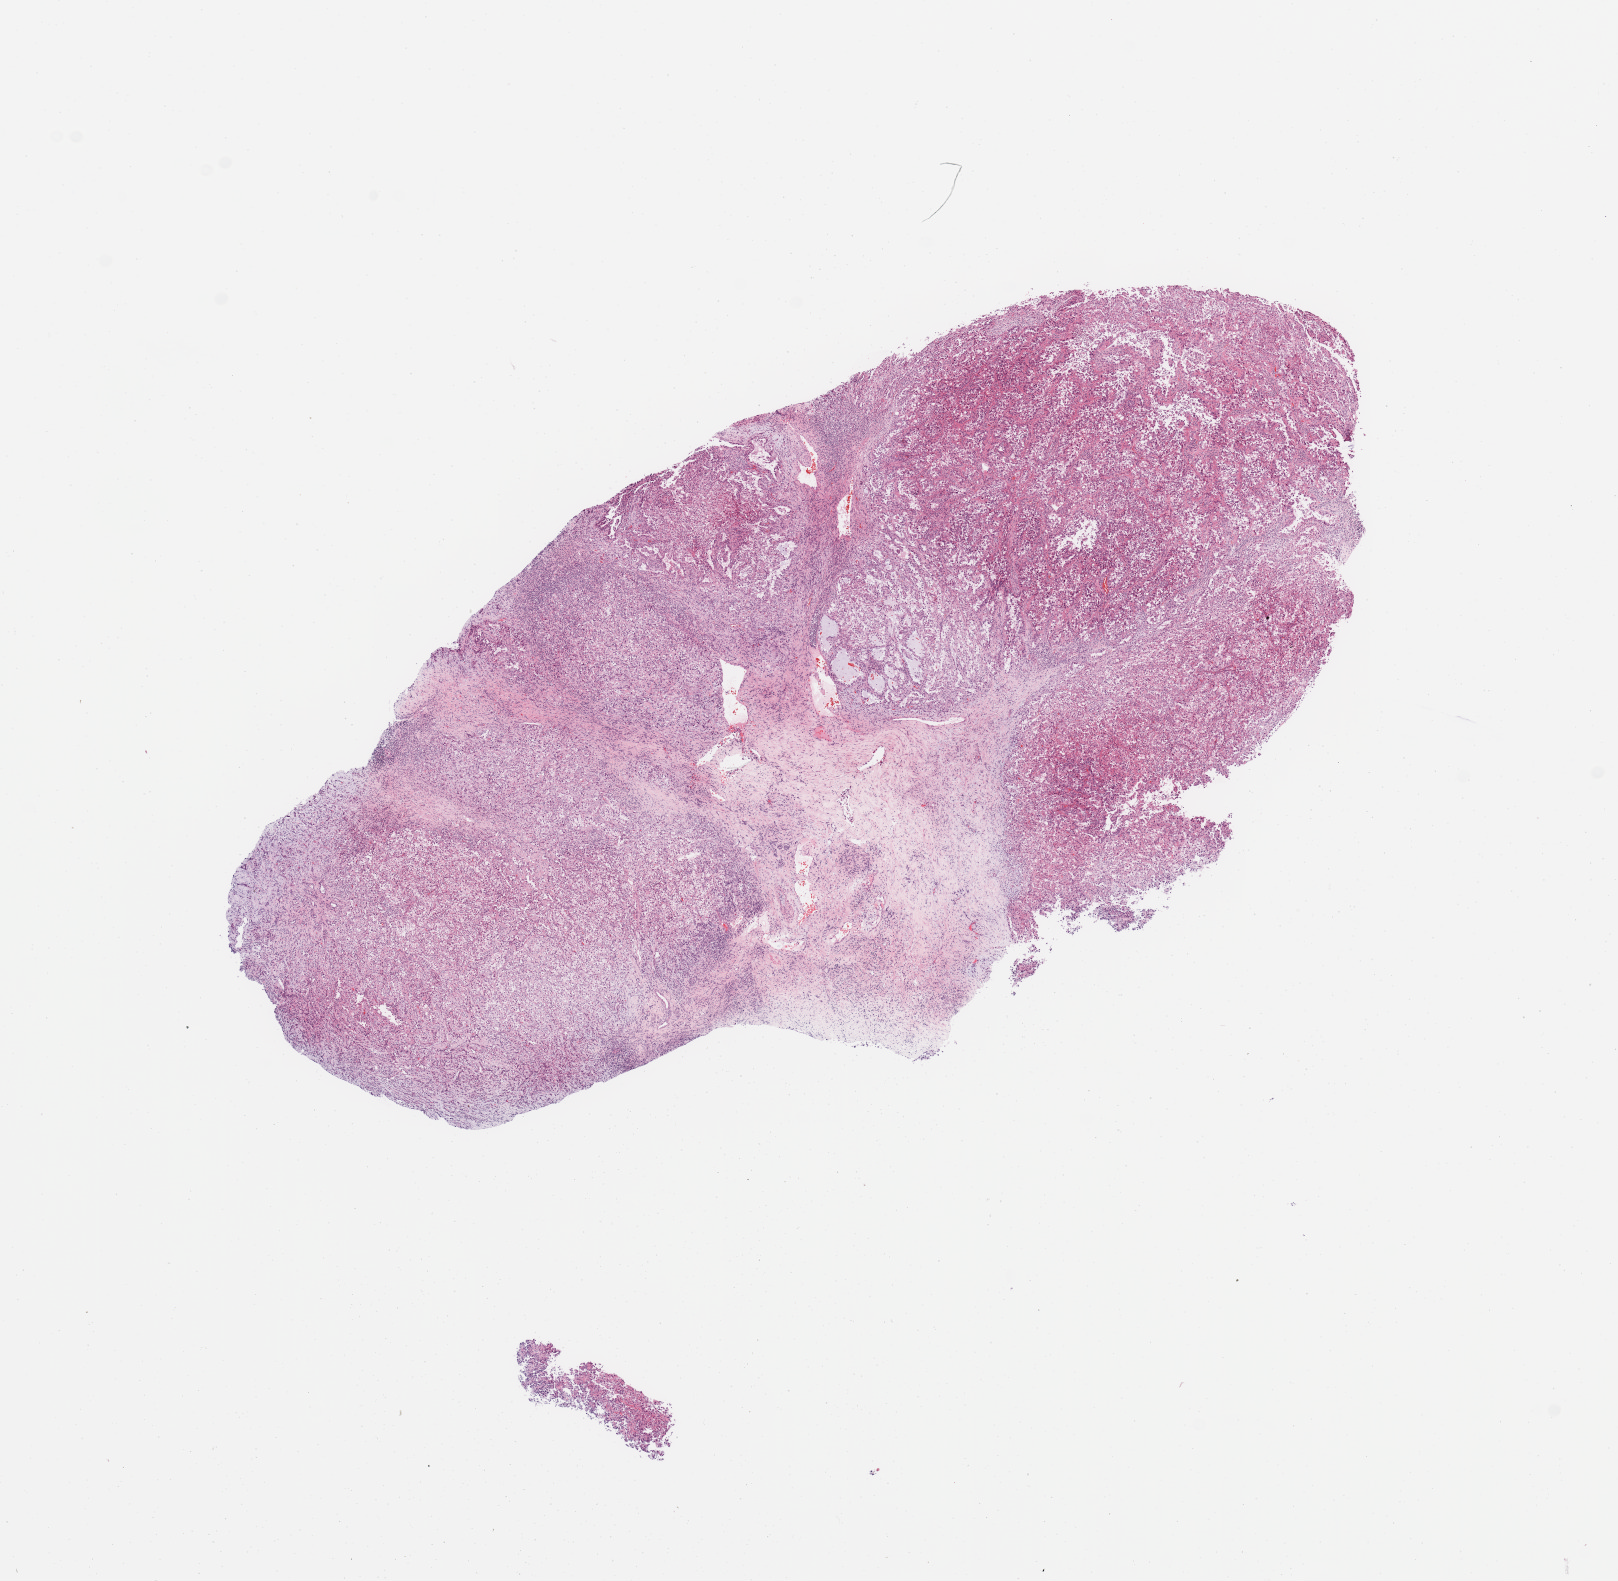
Whole-slide histology image, H&E — shown as a low-resolution overview of the whole scanned area (about 12.8 x 12.5 mm, acquisition: 20x scan). Kidney, tumour tissue. 69-year-old male patient. Histologic grade: G4 (undifferentiated).
Diagnosis: Renal cell carcinoma, NOS. Primary tumour site (as recorded): middle. AJCC pathologic stage: IV.